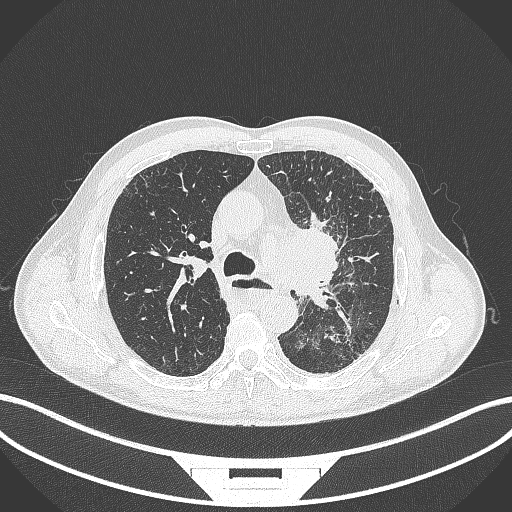
Chest CT, one axial slice; reconstruction kernel B70f; 120 kVp; lung window (W 1500 / L -600 HU); 1 mm slice thickness; 512 × 512 image matrix. Male patient, age 57 years. Case-level facts recorded for this patient, not image findings: clinical TNM (as recorded): T2a N1 M0.
Structures marked on this image (bounding box drawn by a radiologist):
- lung tumour (recorded histology: squamous cell carcinoma): bounding box (x1, y1, x2, y2) in pixels: (287, 216, 338, 311)